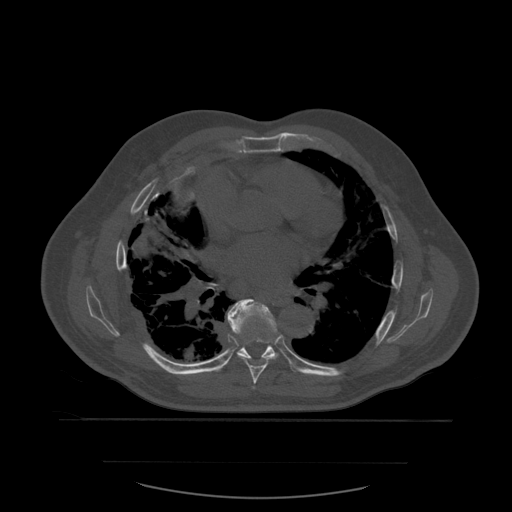
CT including the spine, one axial slice; position 375 of 590 along the scan axis; bone window (W 1800 / L 400 HU); 512 × 512 image matrix, field of view 479 × 479 mm. Patient age 71 years. Case-level facts recorded for this patient, not image findings: primary cancer: lung; vertebrae with lytic lesions (as recorded): T1, T2, L5, S1.
Structures marked on this image (semi-automatically segmented with operator editing):
- T6 vertebra: bounding box (x1, y1, x2, y2) in pixels: (253, 387, 255, 389)
- T7 vertebra: (231, 299, 278, 385)
- T8 vertebra: (227, 309, 279, 361)